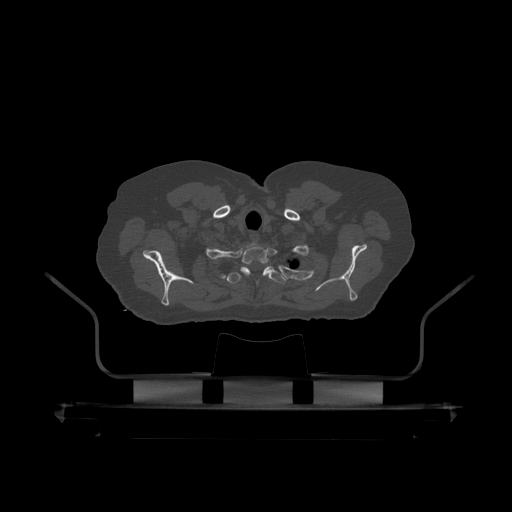
CT including the spine, one axial slice; slice 384 of 390 in the series (ordered by position); reconstruction kernel STANDARD; 120 kVp; bone window (W 1800 / L 400 HU); 1.25 mm slice thickness; 512 × 512 image matrix. Male patient, age 60 years. From the clinical record (not read from this slice): primary cancer: prostate.
Structures marked on this image (semi-automatically segmented with operator editing):
- T1 vertebra: box from (x=214, y=245) to (x=270, y=276) px
- T2 vertebra: (x=227, y=266)–(x=286, y=307)